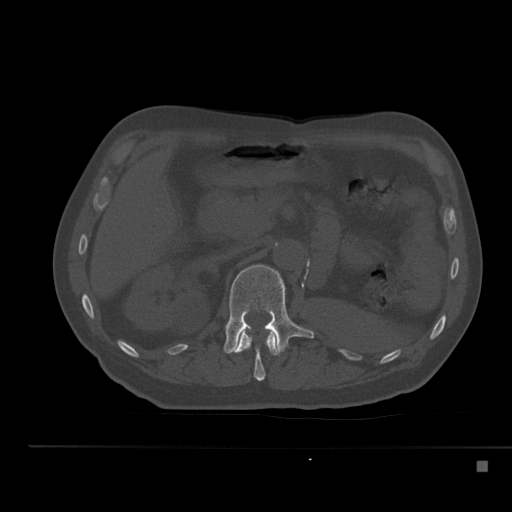
CT including the spine, one axial slice. Position 213 of 517 along the scan axis. Reconstruction kernel Br40s. 120 kVp. Bone window (W 1800 / L 400 HU). 512 × 512 image matrix, field of view 408 × 408 mm. Male patient, age 70 years. Case-level facts recorded for this patient, not image findings: primary cancer: renal; vertebrae with lytic lesions (as recorded): T4, T6, T10, T12, L3, L4, L5.
Outlined on this slice (semi-automatic segmentation, software-assisted and operator-edited):
- L1 vertebra: bounding box (x1, y1, x2, y2) in pixels: (224, 264, 314, 355)
- T12 vertebra: (232, 331, 279, 381)